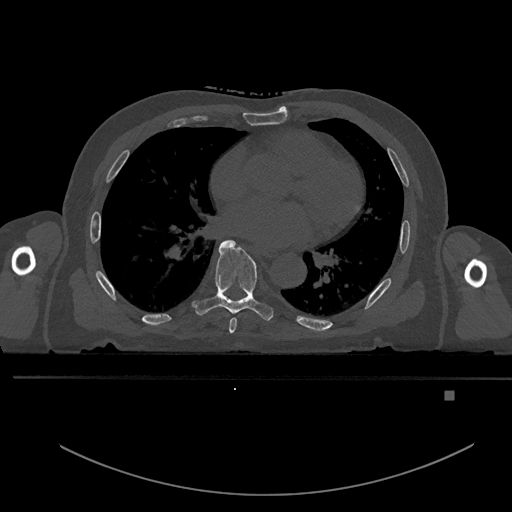
CT including the spine, one axial slice. Slice 258 of 969 in the series (ordered by position). Bone window (W 1800 / L 400 HU). 0.5 mm slice thickness. 512 × 512 image matrix. Patient: male, 82 years. From the clinical record (not read from this slice): primary cancer: prostate; vertebrae with lytic lesions (as recorded): T11, T9, T8, T2.
Structures marked on this image (semi-automatically segmented with operator editing):
- T6 vertebra: bounding box <229,318,237,334> (left, top, right, bottom; pixels)
- T7 vertebra: <192,239,273,321>
- T8 vertebra: <245,295,248,298>